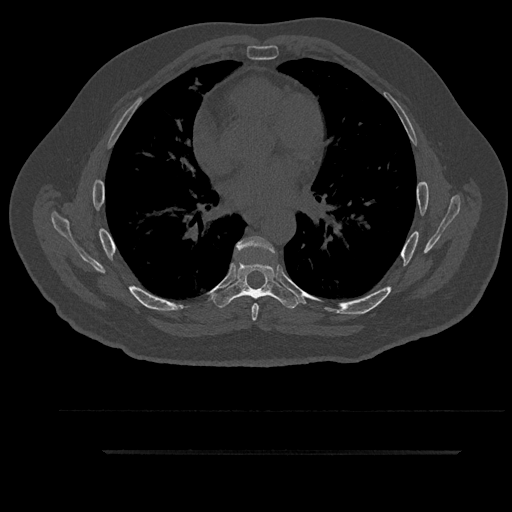
CT including the spine, one axial slice; slice 546 of 797 in the series (ordered by position); reconstruction kernel Br40s/3; 120 kVp; bone window (W 1800 / L 400 HU); 0.5 mm slice thickness; 512 × 512 image matrix, field of view 432 × 432 mm. Male patient, age 63 years. Case-level facts recorded for this patient, not image findings: primary cancer: renal.
Outlined on this slice (semi-automatically segmented with operator editing):
- T6 vertebra: box from (x=236, y=236) to (x=275, y=321) px
- T7 vertebra: (x=212, y=260)–(x=299, y=309)